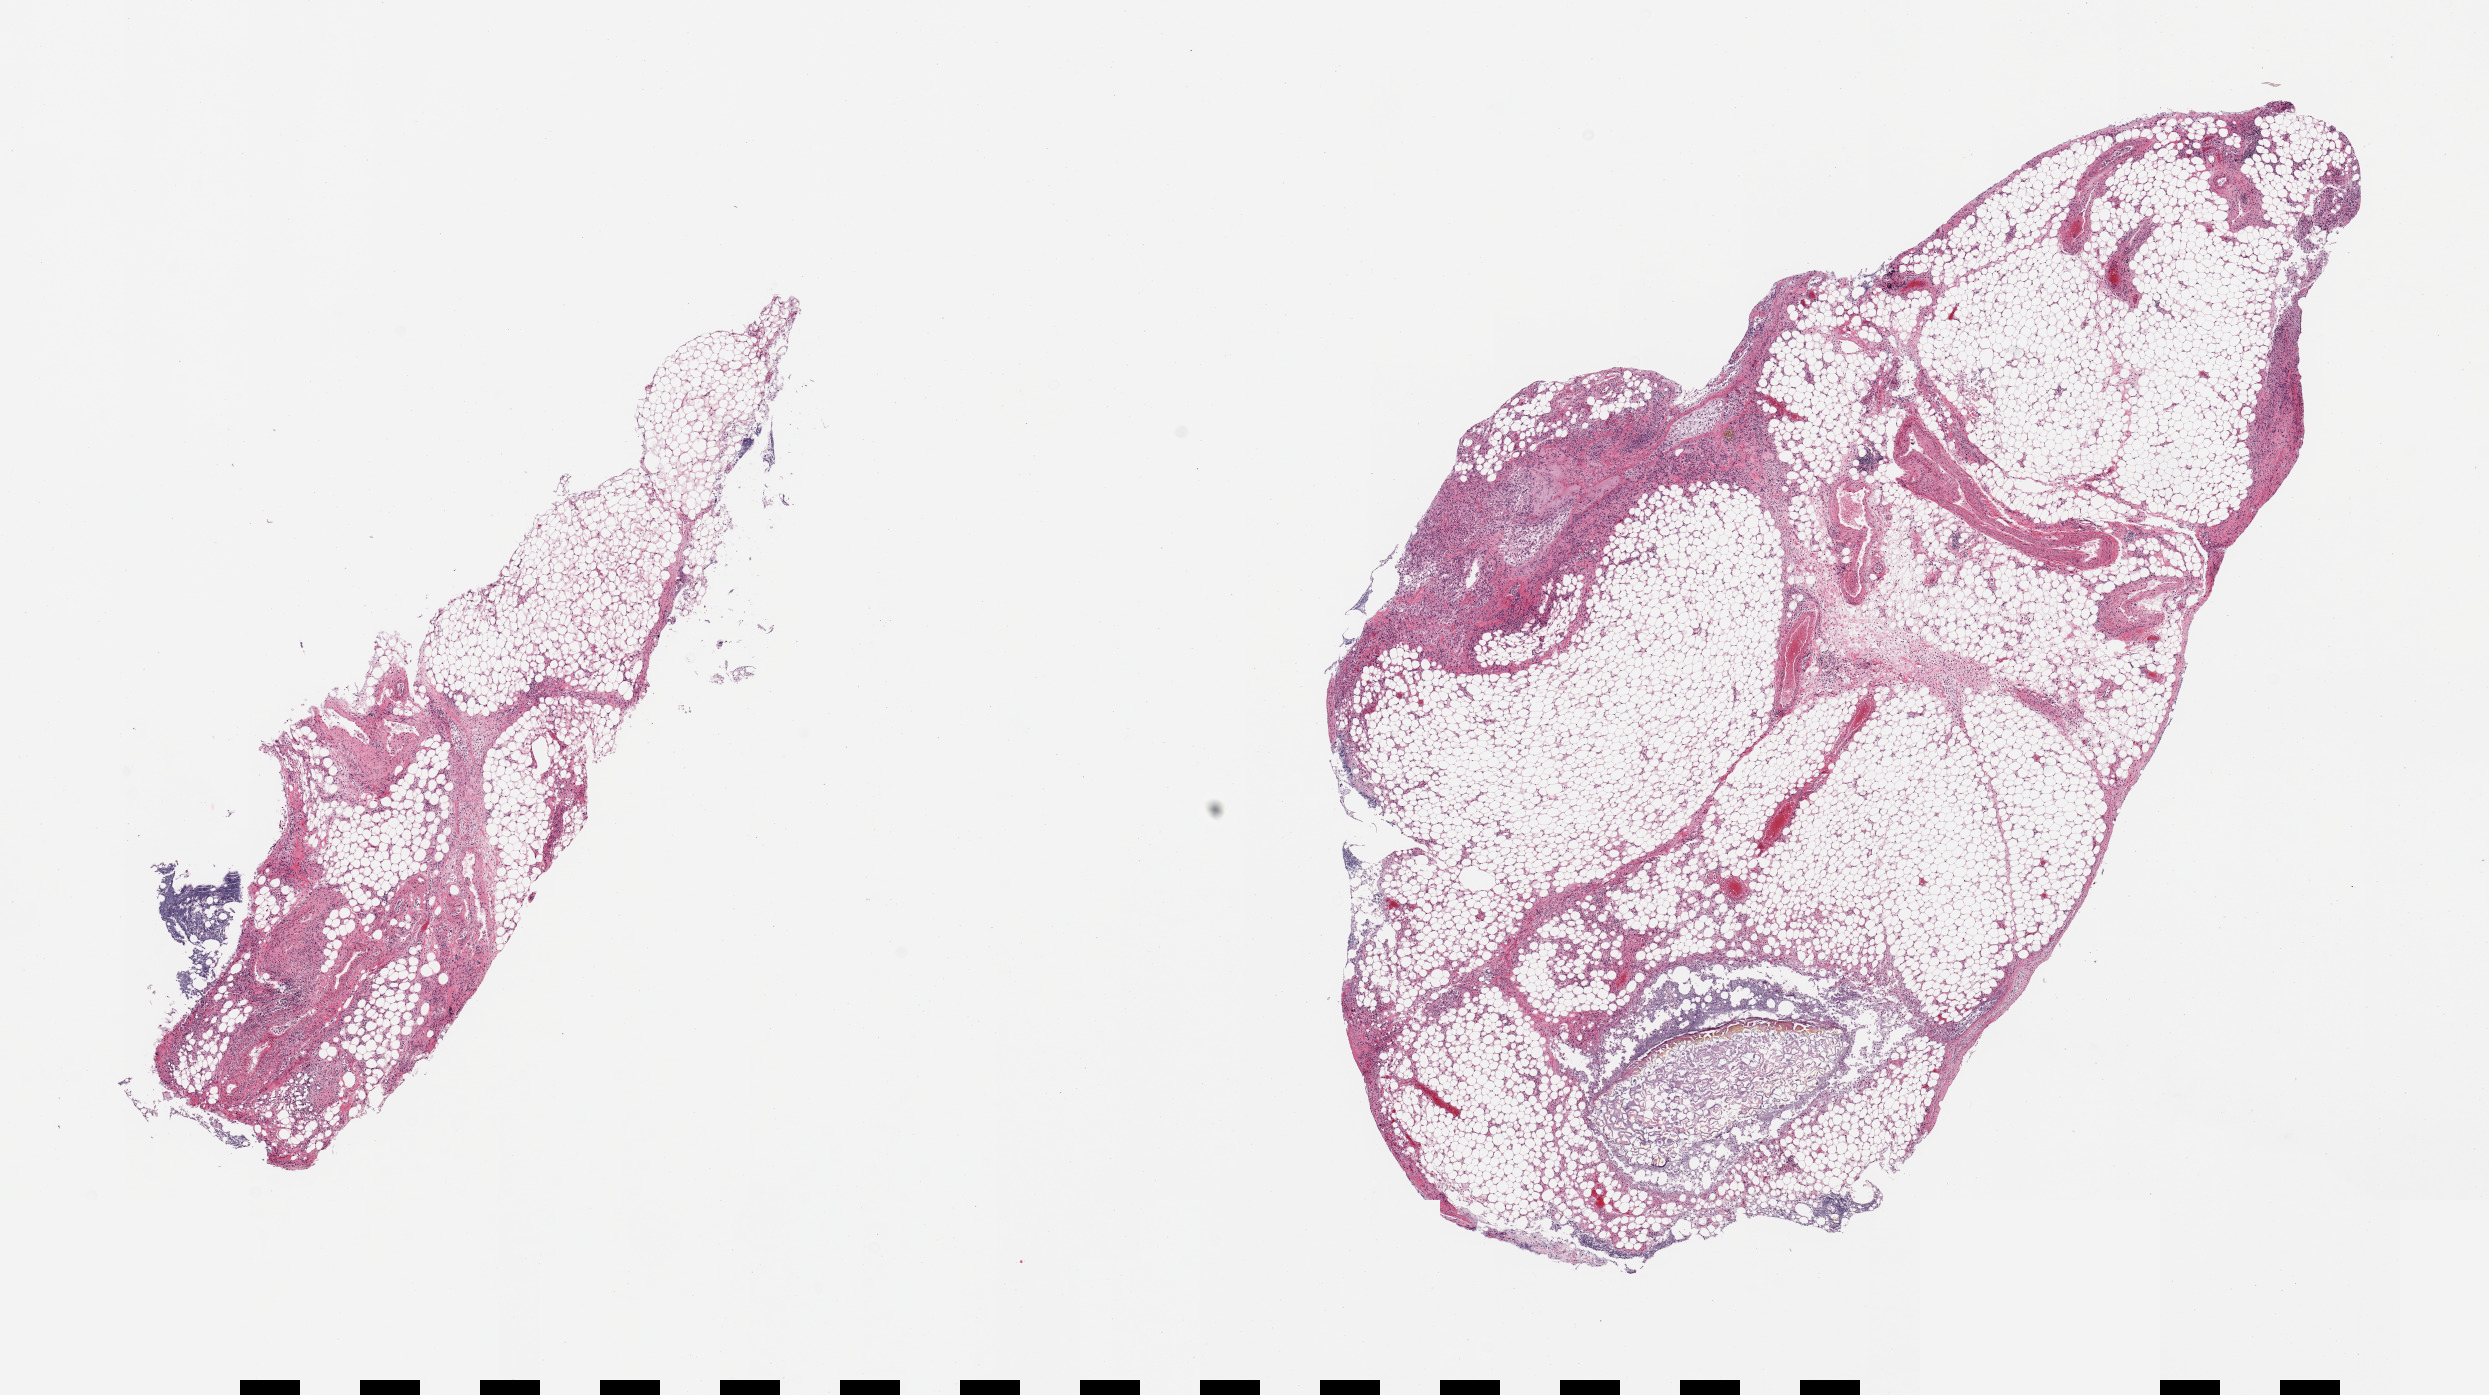
H&E whole-slide image — a low-resolution overview of the entire scanned area, about 19.7 x 11.0 mm; PAXgene-fixed, paraffin-embedded tissue; section of adrenal gland (target tissue); donor tissue sample. Donor sex: male.
Pathologist's review note for this sample: 2 pieces, no adrenal tissue evident, fibroadipose tissue with fat necrosis.